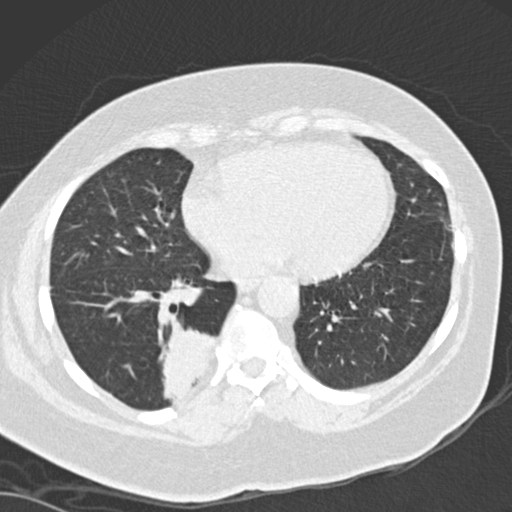
Low-dose screening chest CT, one axial slice. Slice 61 of 162 in the series (ordered by position). Lung window (W 1500 / L -600 HU). 2 mm slice thickness. 512 × 512 image matrix, field of view 328 × 328 mm.
Structures marked on this image (outlined manually by an expert reader):
- lesion 1 (tumor, lower lobe of right lung): bounding box [x1, y1, x2, y2] px = [159, 318, 214, 406]